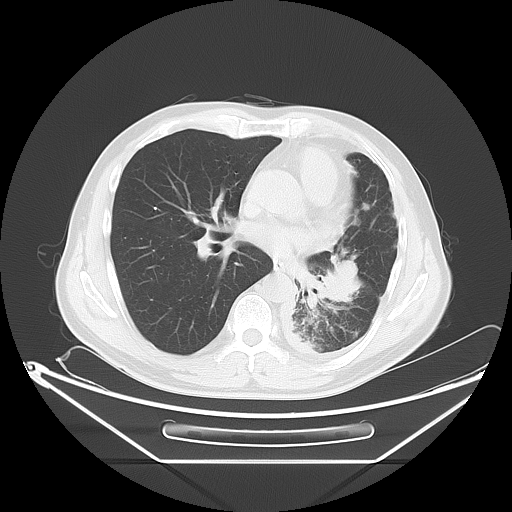
Chest CT, one axial slice. Slice 31 of 63 in the series (ordered by position). 120 kVp. Lung window (W 1500 / L -600 HU). 5 mm slice thickness. 512 × 512 image matrix, field of view 442 × 442 mm. Male patient, age 60 years. Case-level facts recorded for this patient, not image findings: clinical TNM (as recorded): T4 N1 M1.
Structures marked on this image (bounding box drawn by a radiologist):
- lung tumour (recorded histology: adenocarcinoma): bounding box (x1, y1, x2, y2) in pixels: (293, 254, 375, 333)